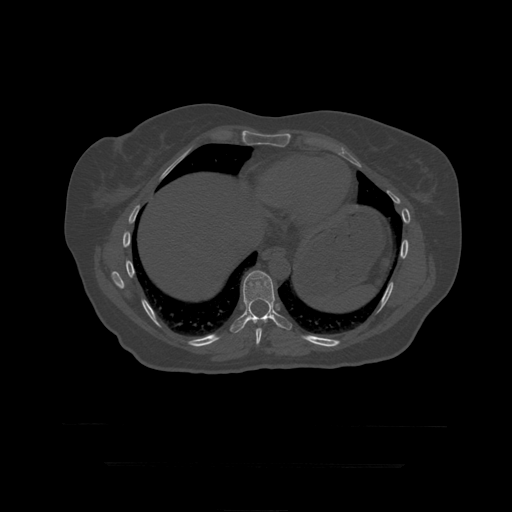
CT including the spine, one axial slice. Position 247 of 399 along the scan axis. Reconstruction kernel STANDARD. 120 kVp. Bone window (W 1800 / L 400 HU). 512 × 512 image matrix. Patient age 41 years. Case-level facts recorded for this patient, not image findings: primary cancer: breast.
Structures marked on this image (semi-automatically segmented with operator editing):
- T10 vertebra: bounding box [x1, y1, x2, y2] px = [230, 271, 292, 334]
- T9 vertebra: [256, 328, 263, 345]